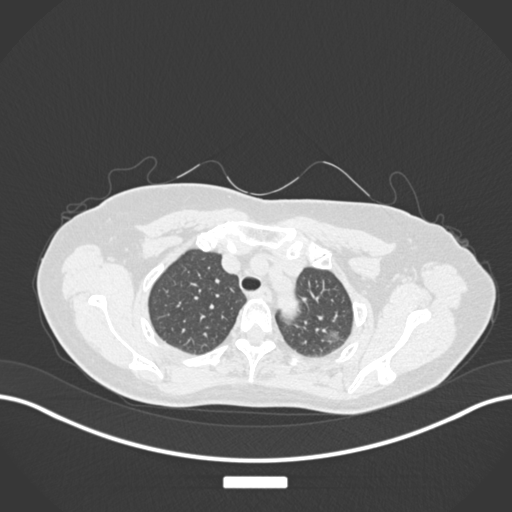
Chest CT, one axial slice. Slice 140 of 181 in the series (ordered by position). Reconstruction kernel B30f. 120 kVp. Lung window (W 1500 / L -600 HU). 1 mm slice thickness. 512 × 512 image matrix, field of view 400 × 400 mm. Female patient, age 58 years. Case-level facts recorded for this patient, not image findings: clinical TNM (as recorded): T1c N0 M0.
Annotated regions visible in this slice (bounding box drawn by a radiologist):
- lung tumour (recorded histology: adenocarcinoma): box from (x=319, y=326) to (x=343, y=348) px